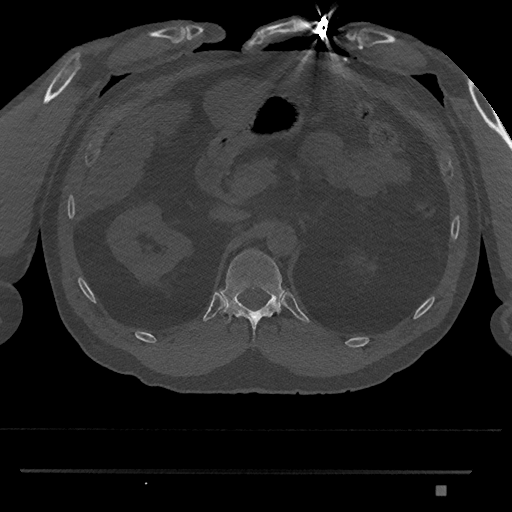
CT including the spine, one axial slice. Position 886 of 1134 along the scan axis. Reconstruction kernel Br40s/3. 120 kVp. Bone window (W 1800 / L 400 HU). 0.5 mm slice thickness. 512 × 512 image matrix, field of view 429 × 429 mm. Patient: male, 65 years. Case-level facts recorded for this patient, not image findings: primary cancer: prostate.
Outlined on this slice (semi-automatically segmented with operator editing):
- T12 vertebra: bounding box [x1, y1, x2, y2] px = [219, 249, 285, 342]